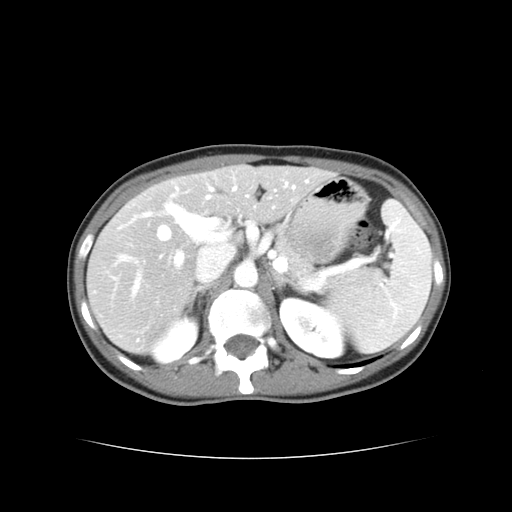
Contrast-enhanced abdominal CT, one axial slice; 120 kVp; intravenous contrast given; soft-tissue window (W 400 / L 40 HU); 512 × 512 image matrix. Female patient, age 54 years. Case-level facts recorded for this patient, not image findings: diagnosis: colorectal cancer liver metastases, imaged before liver resection; multiple liver metastases: yes; largest metastasis: 1.1 cm; disease in both lobes: yes.
Annotated regions visible in this slice (manually delineated by an expert):
- hepatic veins: bounding box [x1, y1, x2, y2] px = [159, 187, 295, 240]
- liver: [89, 166, 325, 351]
- planned liver remnant (the part of the liver to remain after resection): [214, 166, 325, 222]
- portal vein (with intrahepatic branches): [144, 181, 308, 264]